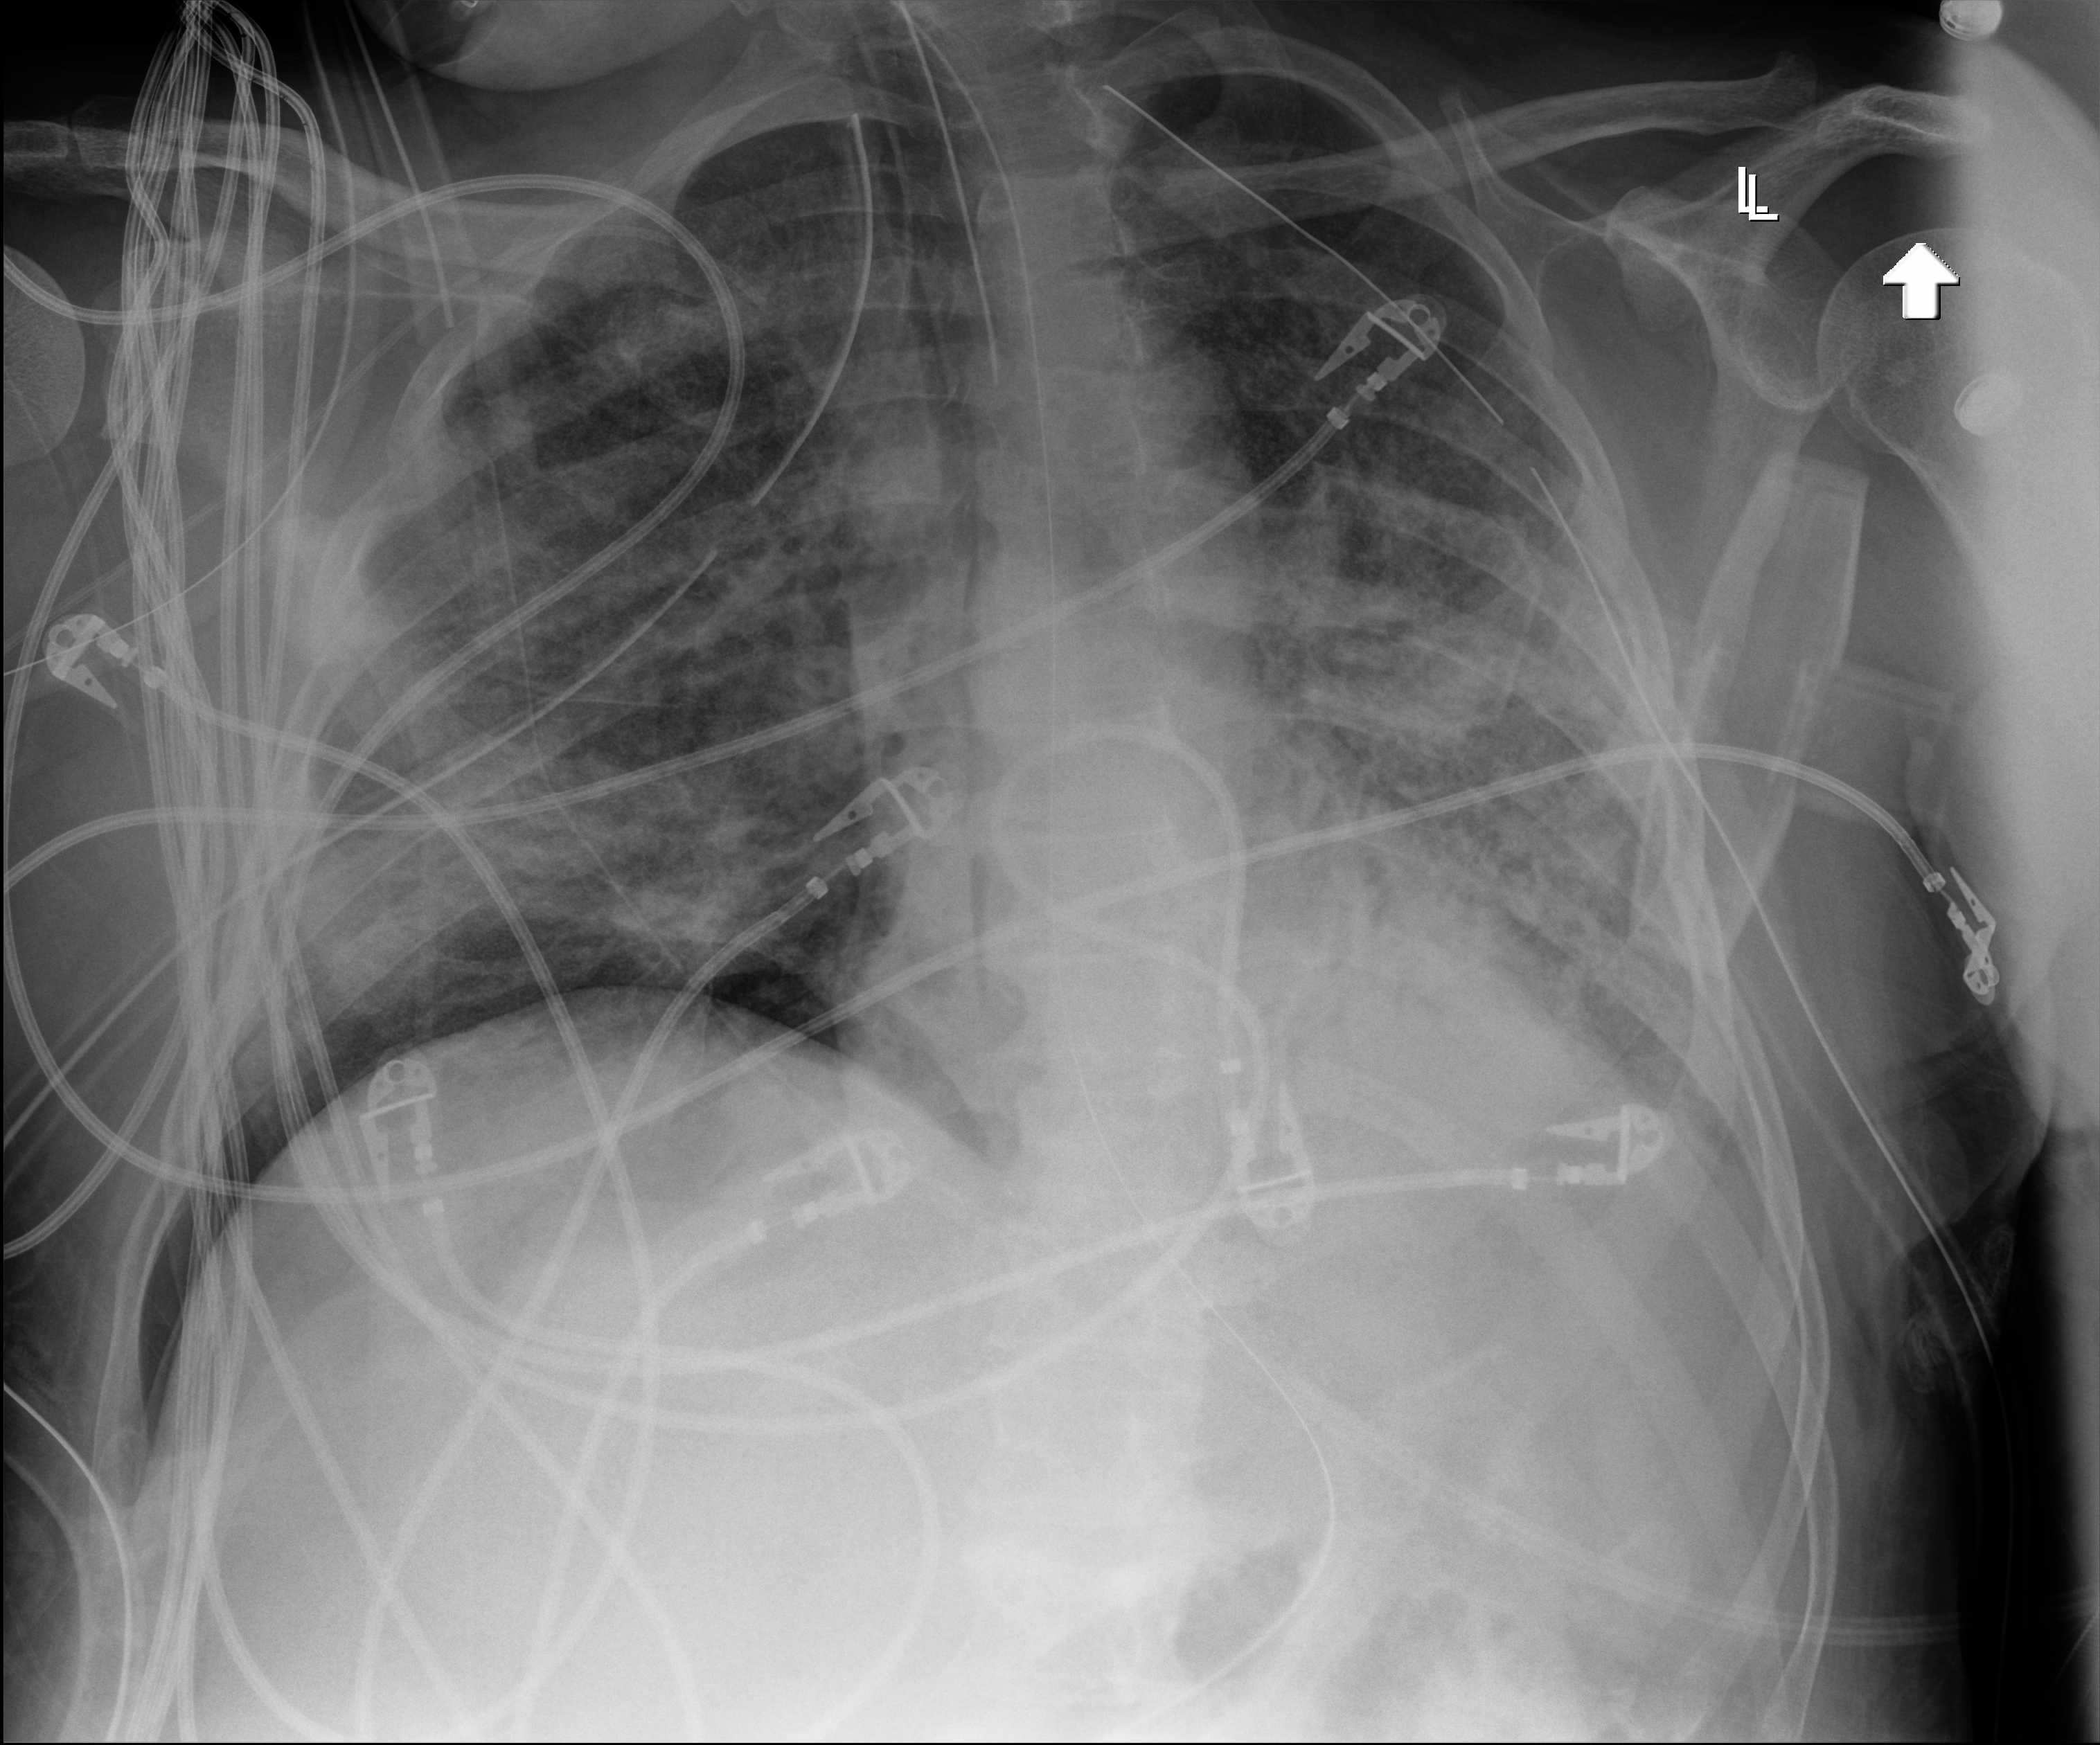
Portable chest radiograph; anteroposterior (AP) projection. Patient hospitalised with COVID-19; male, aged 18–59 years.
Admission-level facts for this patient (not findings on this image; timing relative to this image not recorded): length of hospital stay: 83 days; mechanically ventilated during this hospital stay: yes.